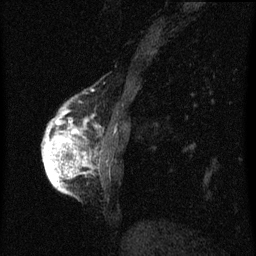
Breast MRI (dynamic contrast-enhanced), one sagittal slice. Position 16 of 60 along the scan axis. Dynamic contrast-enhanced series, image 2 of 3 at this slice position (ordered by acquisition). 1.5 T. TE 4.2 ms, TR 8 ms. 2 mm slice thickness. 256 × 256 image matrix, field of view 180 × 180 mm. Female patient, age 56 years.
Outlined on this slice (semi-automatically segmented with operator editing):
- analysis volume of interest (the breast-tissue region the enhancement analysis was run in; not a lesion): bounding box [x1, y1, x2, y2] px = [44, 110, 105, 193]
- tumour enhancement mask (voxels above the 70 % enhancement threshold inside the analysis volume of interest): [44, 118, 89, 193]